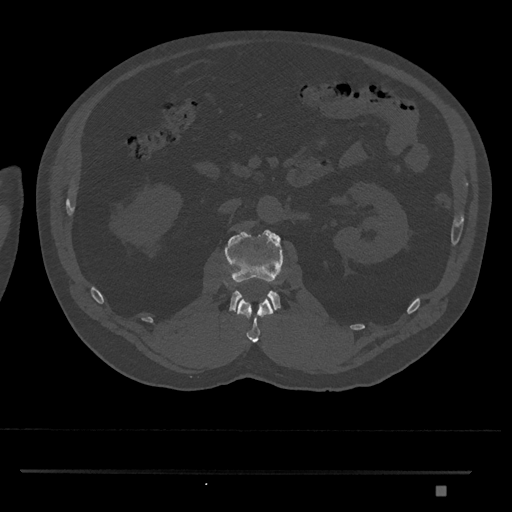
CT including the spine, one axial slice; slice 786 of 1134 in the series (ordered by position); bone window (W 1800 / L 400 HU); 0.5 mm slice thickness; 512 × 512 image matrix, field of view 429 × 429 mm. Male patient, age 65 years. Case-level facts recorded for this patient, not image findings: primary cancer: prostate.
Outlined on this slice (semi-automatic segmentation, software-assisted and operator-edited):
- L1 vertebra: bounding box (x1, y1, x2, y2) in pixels: (237, 298, 275, 343)
- L2 vertebra: (224, 229, 285, 312)